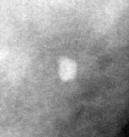
Cropped region of a digitized screen-film mammogram centred on a radiologist-marked abnormality, left breast, MLO view, BI-RADS breast density category 3 (scale 1–4).
- Finding: calcifications, morphology round and regular / lucent centered; BI-RADS assessment category 2; subtlety rating 3 on a 1 (subtle) to 5 (obvious) scale; benign; no additional work-up was recommended (benign without callback).